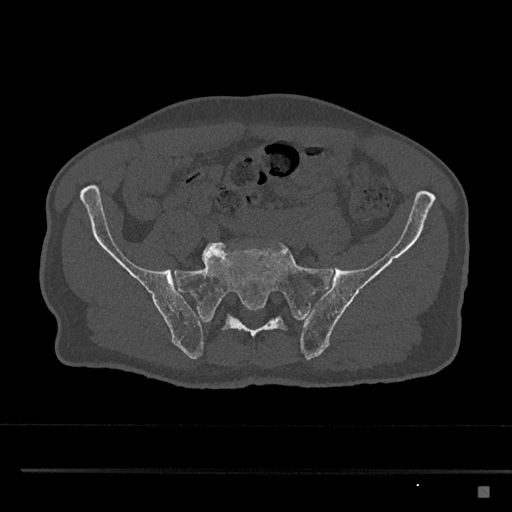
CT including the spine, one axial slice; position 523 of 797 along the scan axis; reconstruction kernel Br40s/3; bone window (W 1800 / L 400 HU); 0.5 mm slice thickness; 512 × 512 image matrix, field of view 391 × 391 mm. Patient: male, 59 years. From the clinical record (not read from this slice): primary cancer: prostate.
Structures marked on this image (semi-automatic segmentation, software-assisted and operator-edited):
- L5 vertebra: bounding box (x1, y1, x2, y2) in pixels: (201, 242, 267, 264)